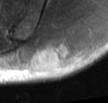
MRI of an extremity soft-tissue mass, one axial slice; position 14 of 42 along the scan axis; T2-weighted fat-saturated; MR volume resampled by the dataset authors to the PET/CT grid (not the native acquisition matrix); 3.27 mm slice thickness; 108 × 103 image matrix, field of view 105 × 101 mm. Male patient. Case-level facts recorded for this patient, not image findings: histological type: leiomyosarcoma; grade: intermediate; site of the primary tumour: left pelvis.
Outlined on this slice (expert contour drawn on MRI and transferred to this co-registered scan by the dataset authors):
- gross tumour volume (mass): box from (x=32, y=42) to (x=70, y=75) px